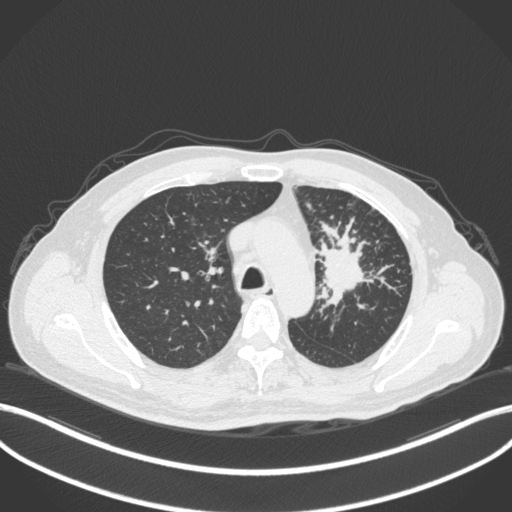
Chest CT, one axial slice. Position 254 of 386 along the scan axis. Reconstruction kernel B31f. Lung window (W 1500 / L -600 HU). 512 × 512 image matrix, field of view 400 × 400 mm. Patient: male, 69 years. Case-level facts recorded for this patient, not image findings: clinical TNM (as recorded): T2a N2 M0.
Annotated regions visible in this slice (bounding box drawn by a radiologist):
- lung tumour (recorded histology: adenocarcinoma): box from (x=313, y=221) to (x=373, y=305) px